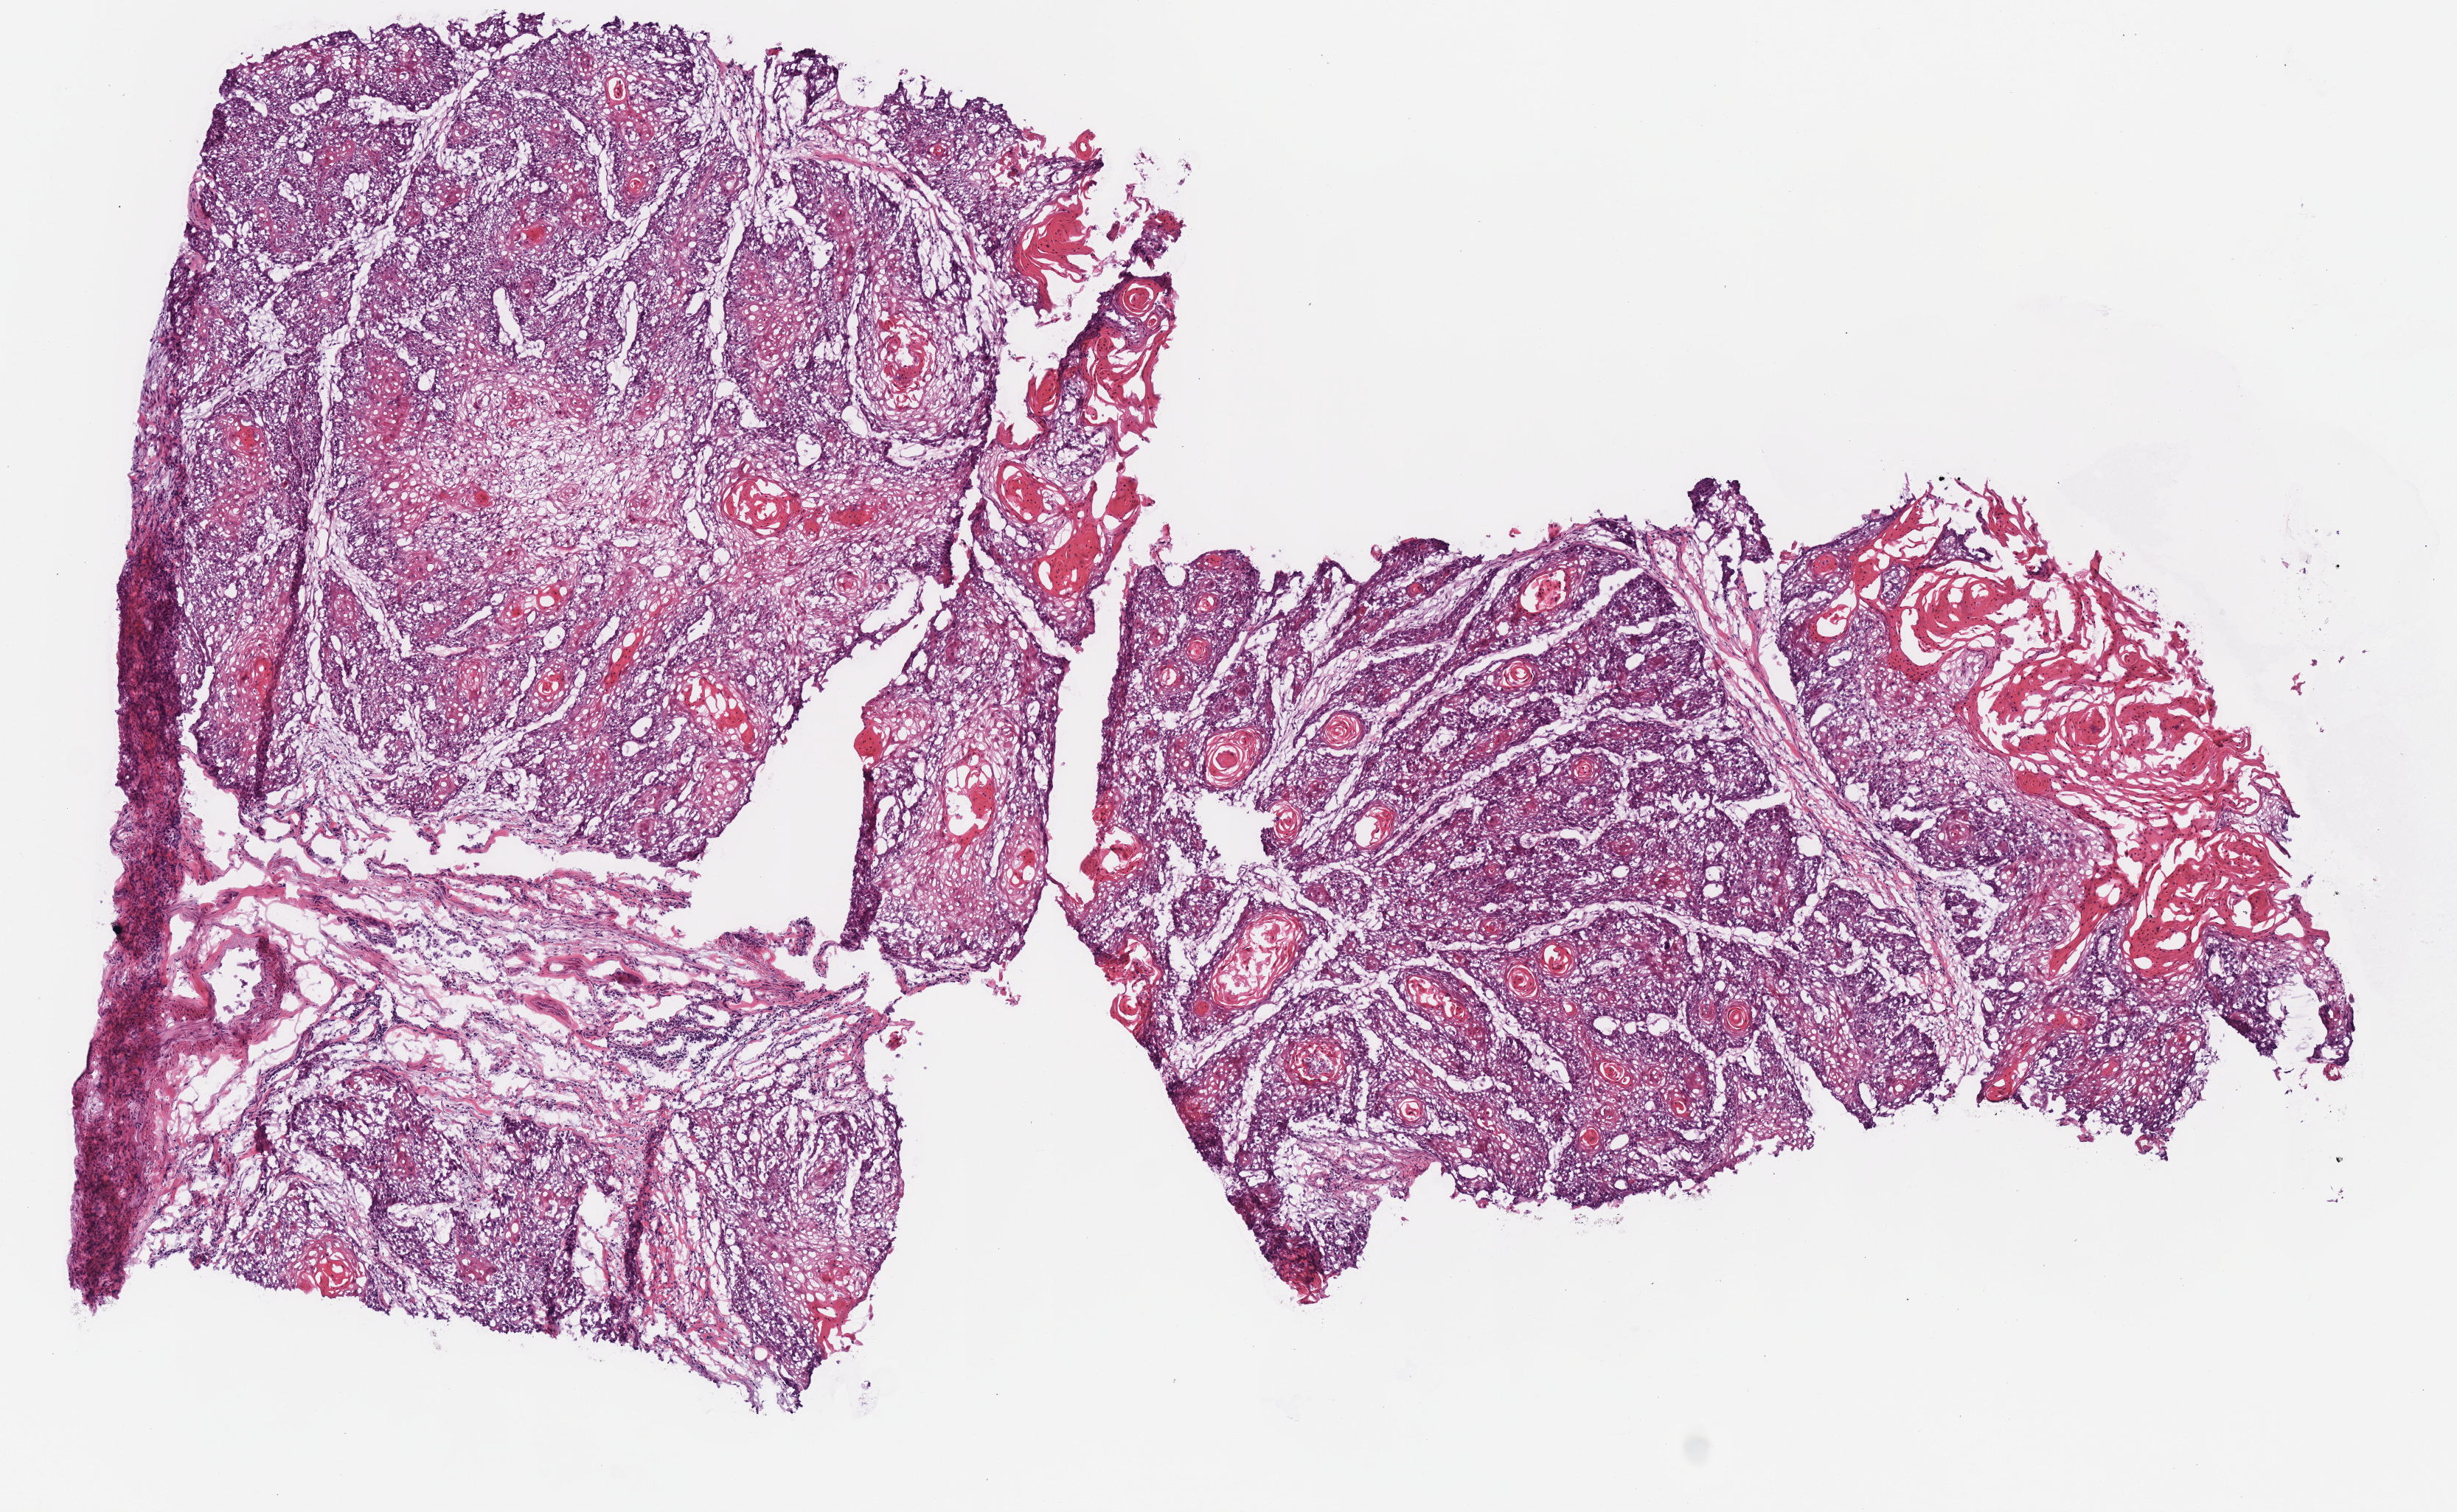
Hematoxylin and eosin (H&E) stained whole-slide image, whole scanned area (about 6.6 x 4.0 mm) shown as a low-resolution overview. Frozen section from the top of the tissue portion. Head and neck, primary tumour sample. Male, age 47 years at initial diagnosis. Histologic grade: G2 (moderately differentiated). Pathologist review of this section (percent, as recorded): tumour cells 100%, tumour nuclei 80%, normal cells 0%, stromal cells 0%, necrosis 0%. Infiltration values recorded for this section: lymphocyte infiltration 10%, monocyte infiltration 0%, neutrophil infiltration 0%.
- histologic diagnosis: Squamous cell carcinoma, NOS (overlapping lesion of lip, oral cavity and pharynx)
- lymph nodes positive (case pathology): 2 of 10 examined
- TNM: T4a N2b
- AJCC pathologic stage: IVA
- laterality: right